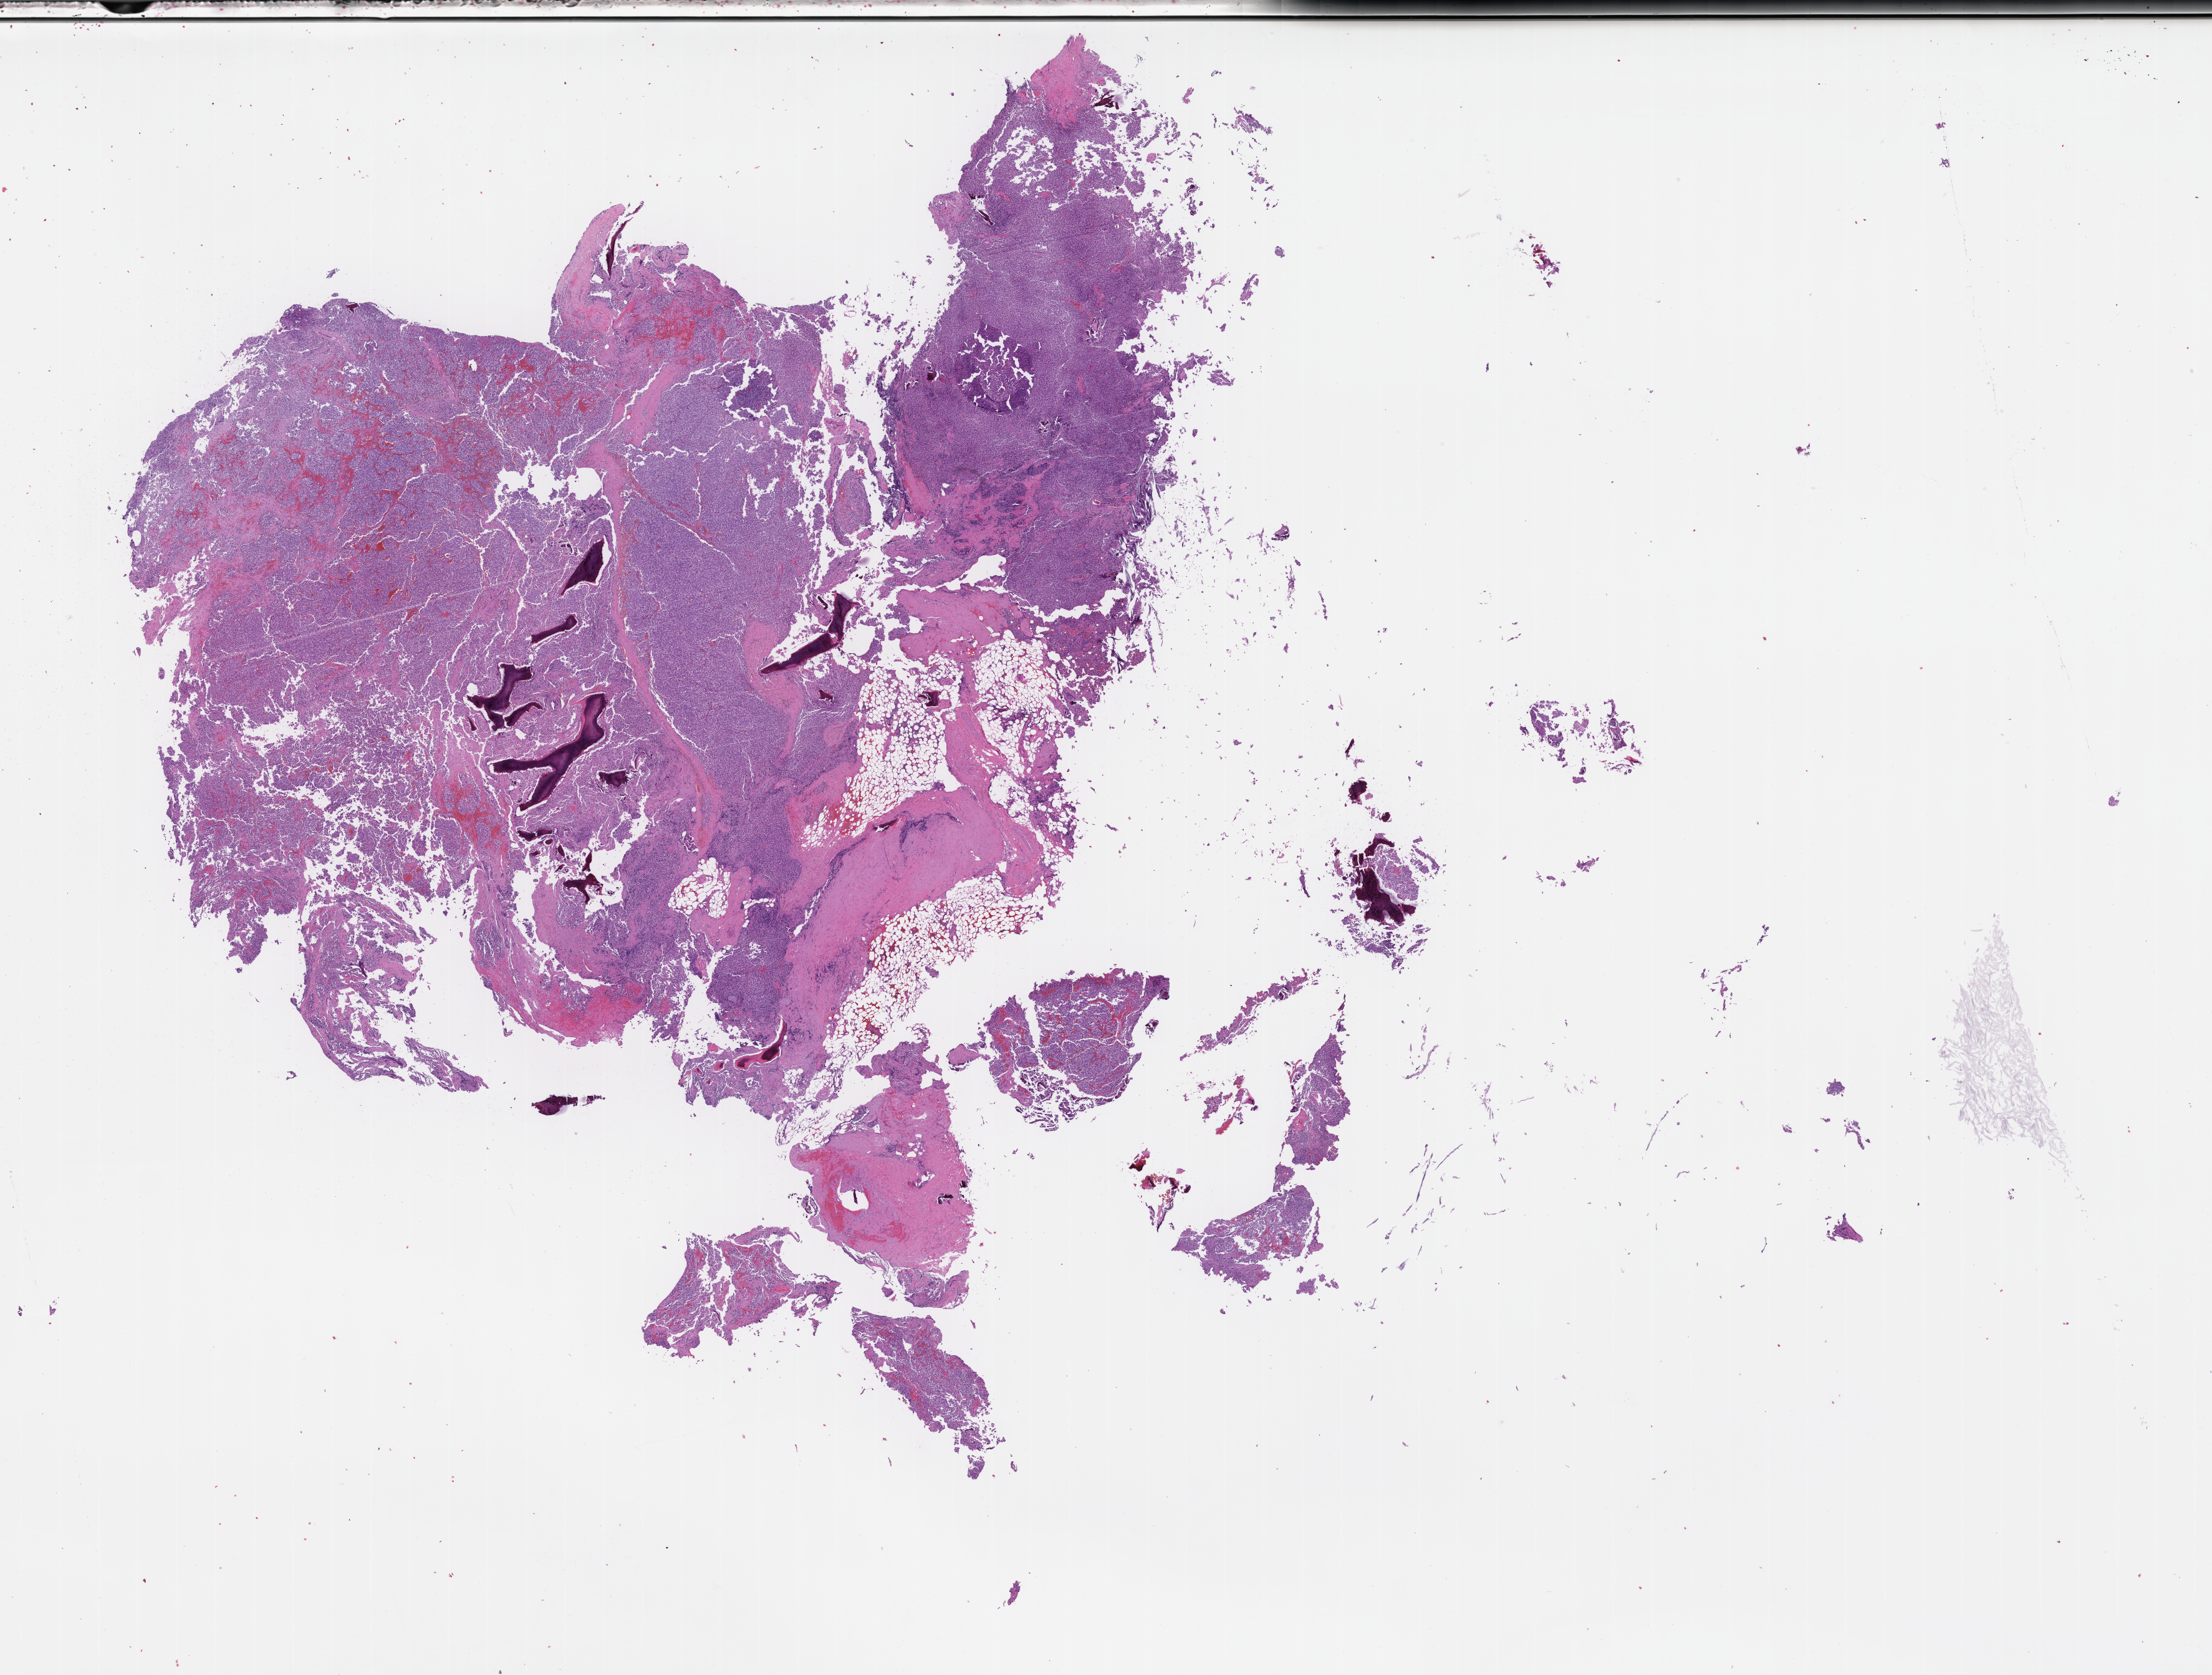
Whole-slide image, haematoxylin and eosin stain, low-resolution overview of the scanned area, about 28.6 x 21.7 mm; formalin-fixed, paraffin-embedded (FFPE) tissue; site: prostate; archival tissue. Patient: male.
• this section: primary tumor
• diagnosis: Prostate Carcinoma